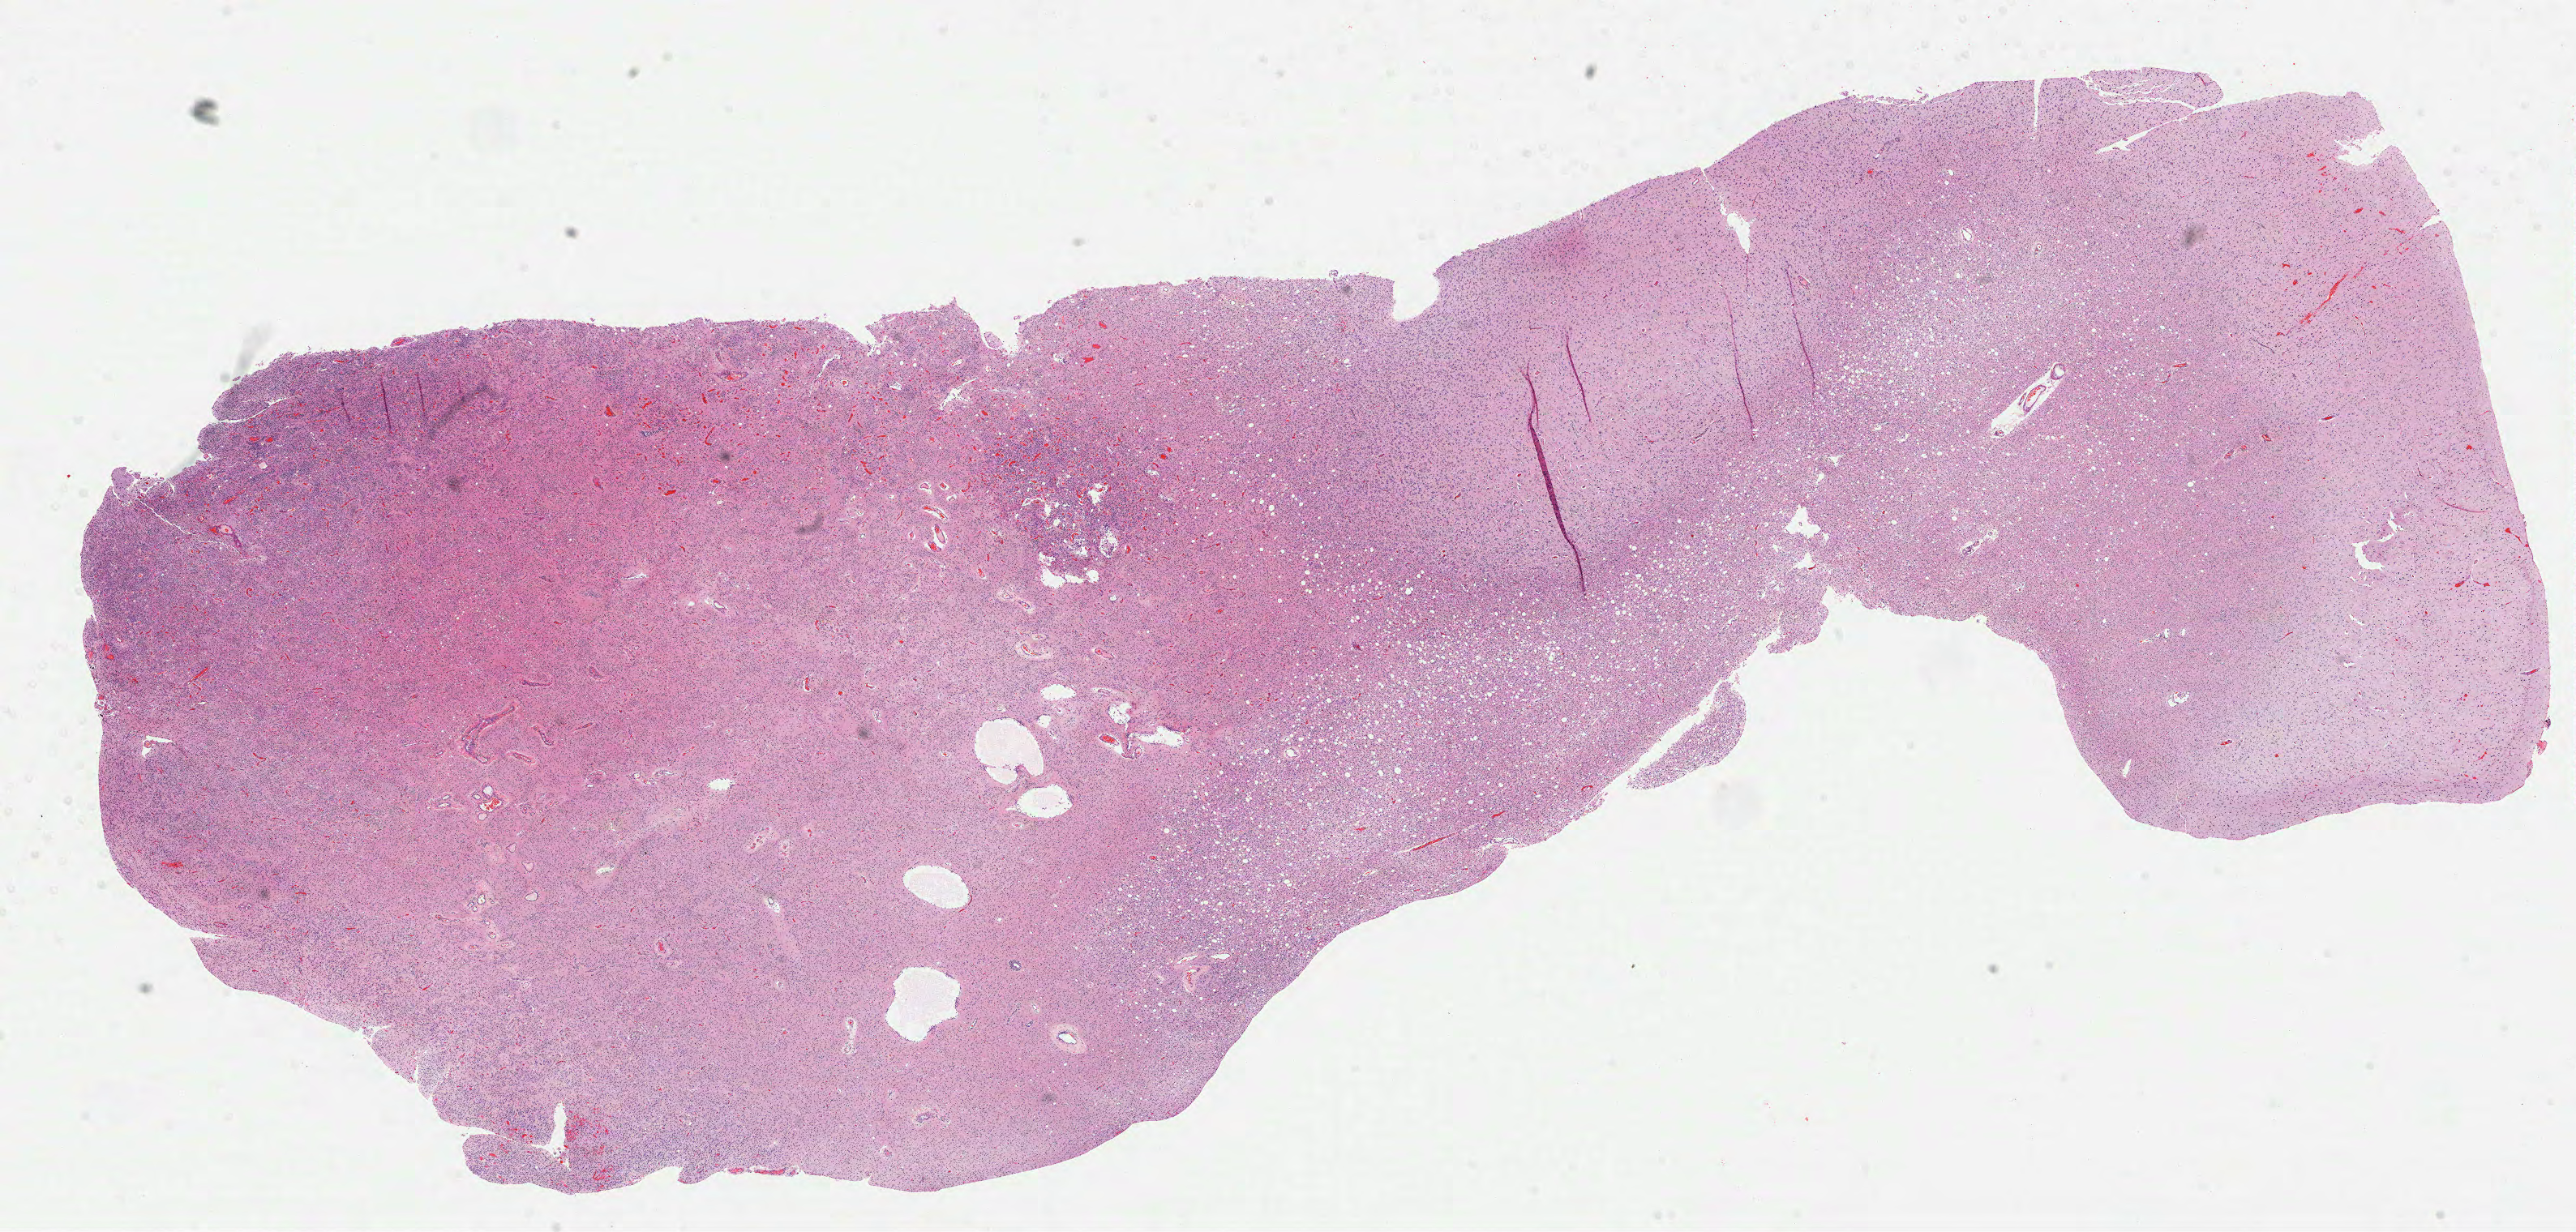
Digitized H&E-stained tissue section (whole slide) — shown as a low-resolution overview of the whole scanned area (about 25.6 x 12.3 mm), formalin-fixed paraffin-embedded (FFPE) diagnostic section, brain, primary tumour sample. Female, age 31 years at initial diagnosis. Histologic grade: G3 (poorly differentiated).
- laterality: left
- diagnosis: Oligodendroglioma, anaplastic (cerebrum)